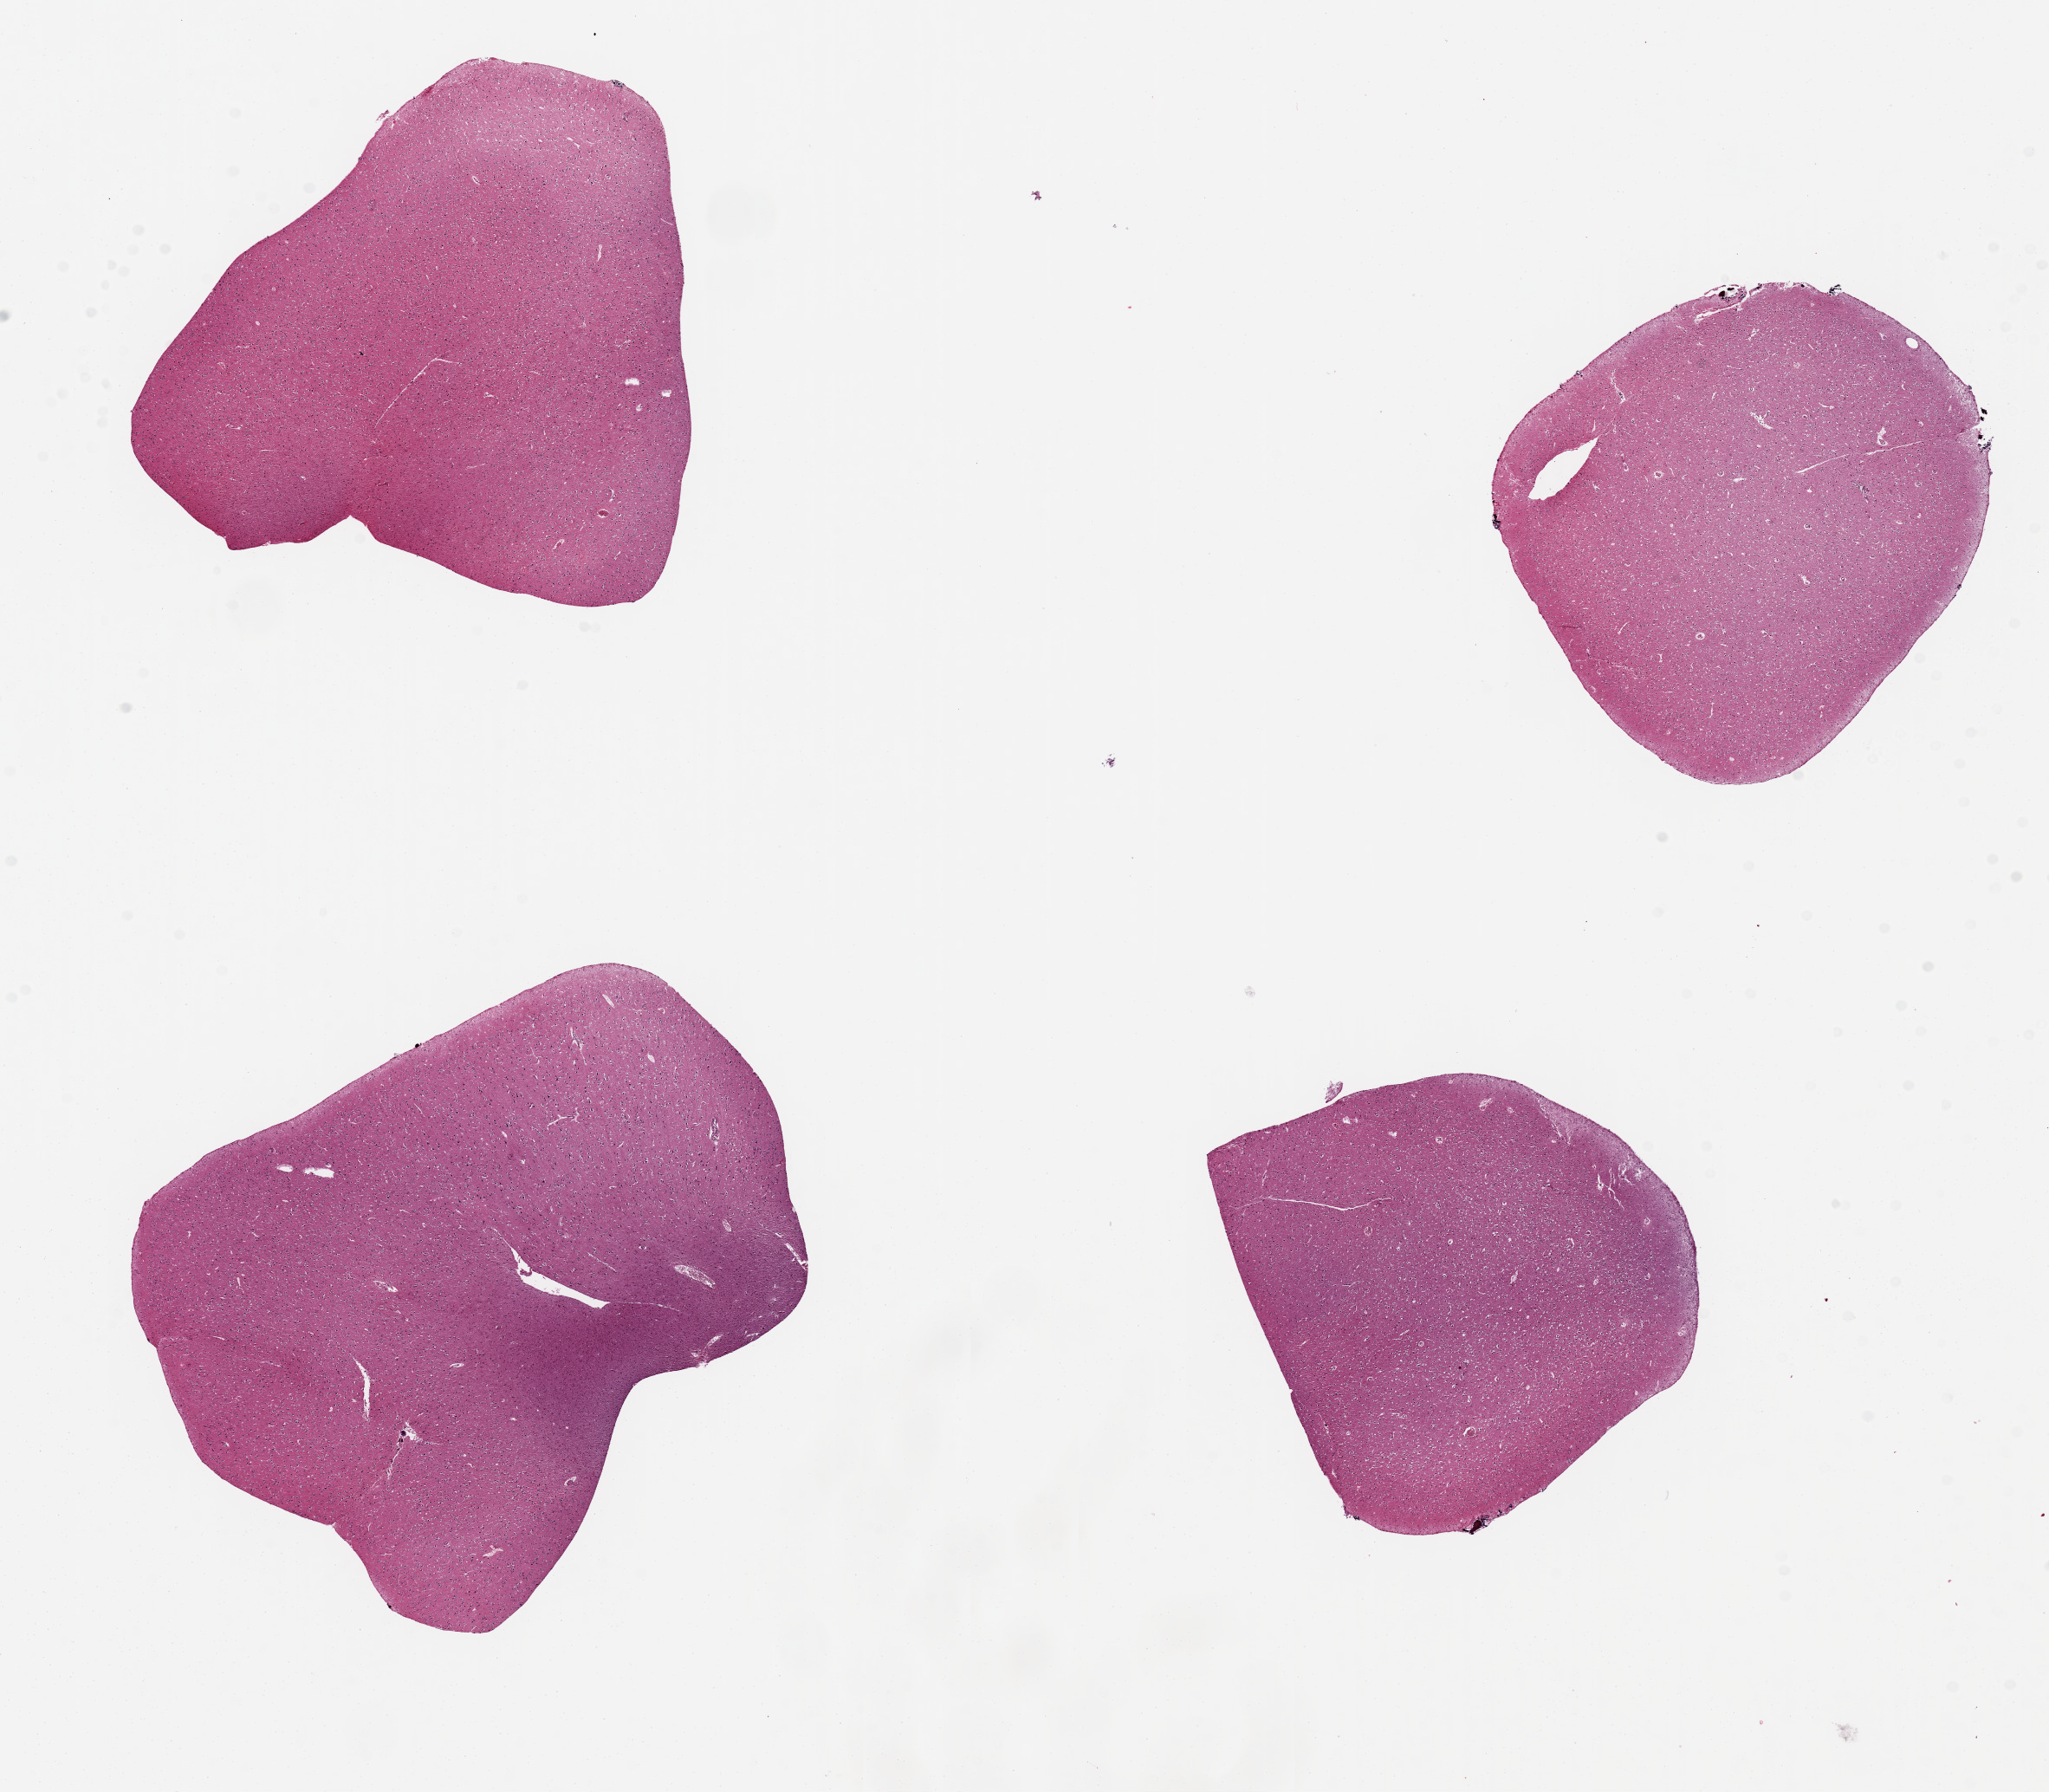
Digitized haematoxylin and eosin-stained section, whole scanned area (about 18.7 x 16.4 mm) shown as a low-resolution overview; PAXgene-fixed paraffin-embedded (PFPE) section; section of cerebral cortex (target tissue); tissue donor sample. Female donor.
- reviewer comment on this tissue sample: 4 pieces, ~5x5mm